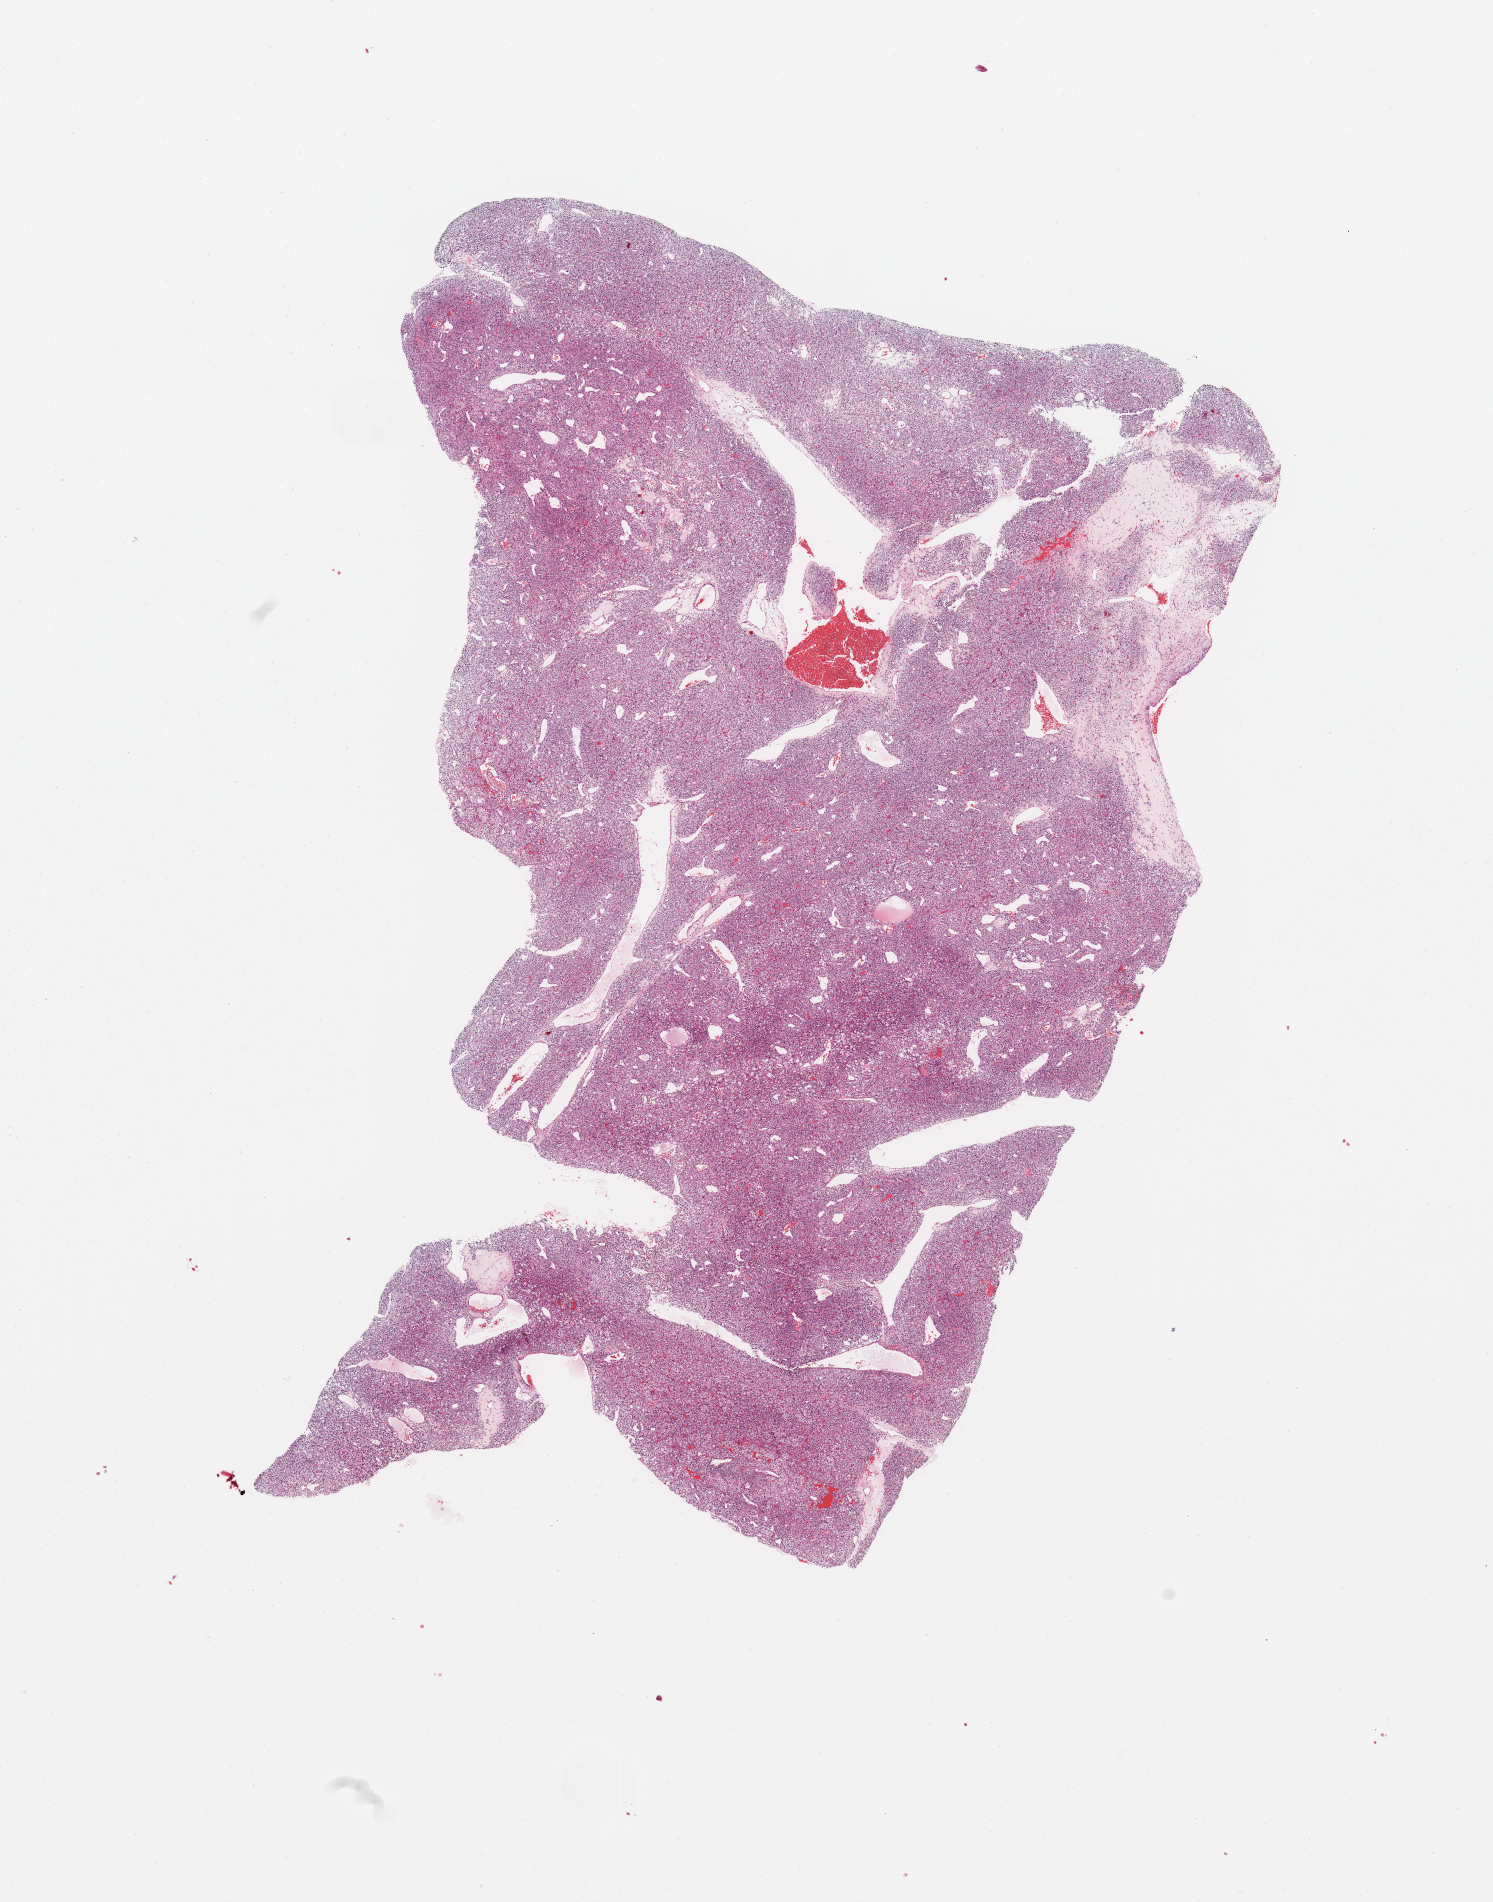
Whole-slide histology image, H&E — shown as a low-resolution overview of the whole scanned area (about 11.8 x 15.0 mm); tumour tissue sample, sampled site: kidney. 89-year-old male patient. Histologic grade: G2 (moderately differentiated). Composition of this section per pathologist review: tumour nuclei 95%, necrosis 0%.
* primary tumour site (as recorded): lower pole
* AJCC pathologic stage: III
* diagnosis: Renal cell carcinoma, NOS